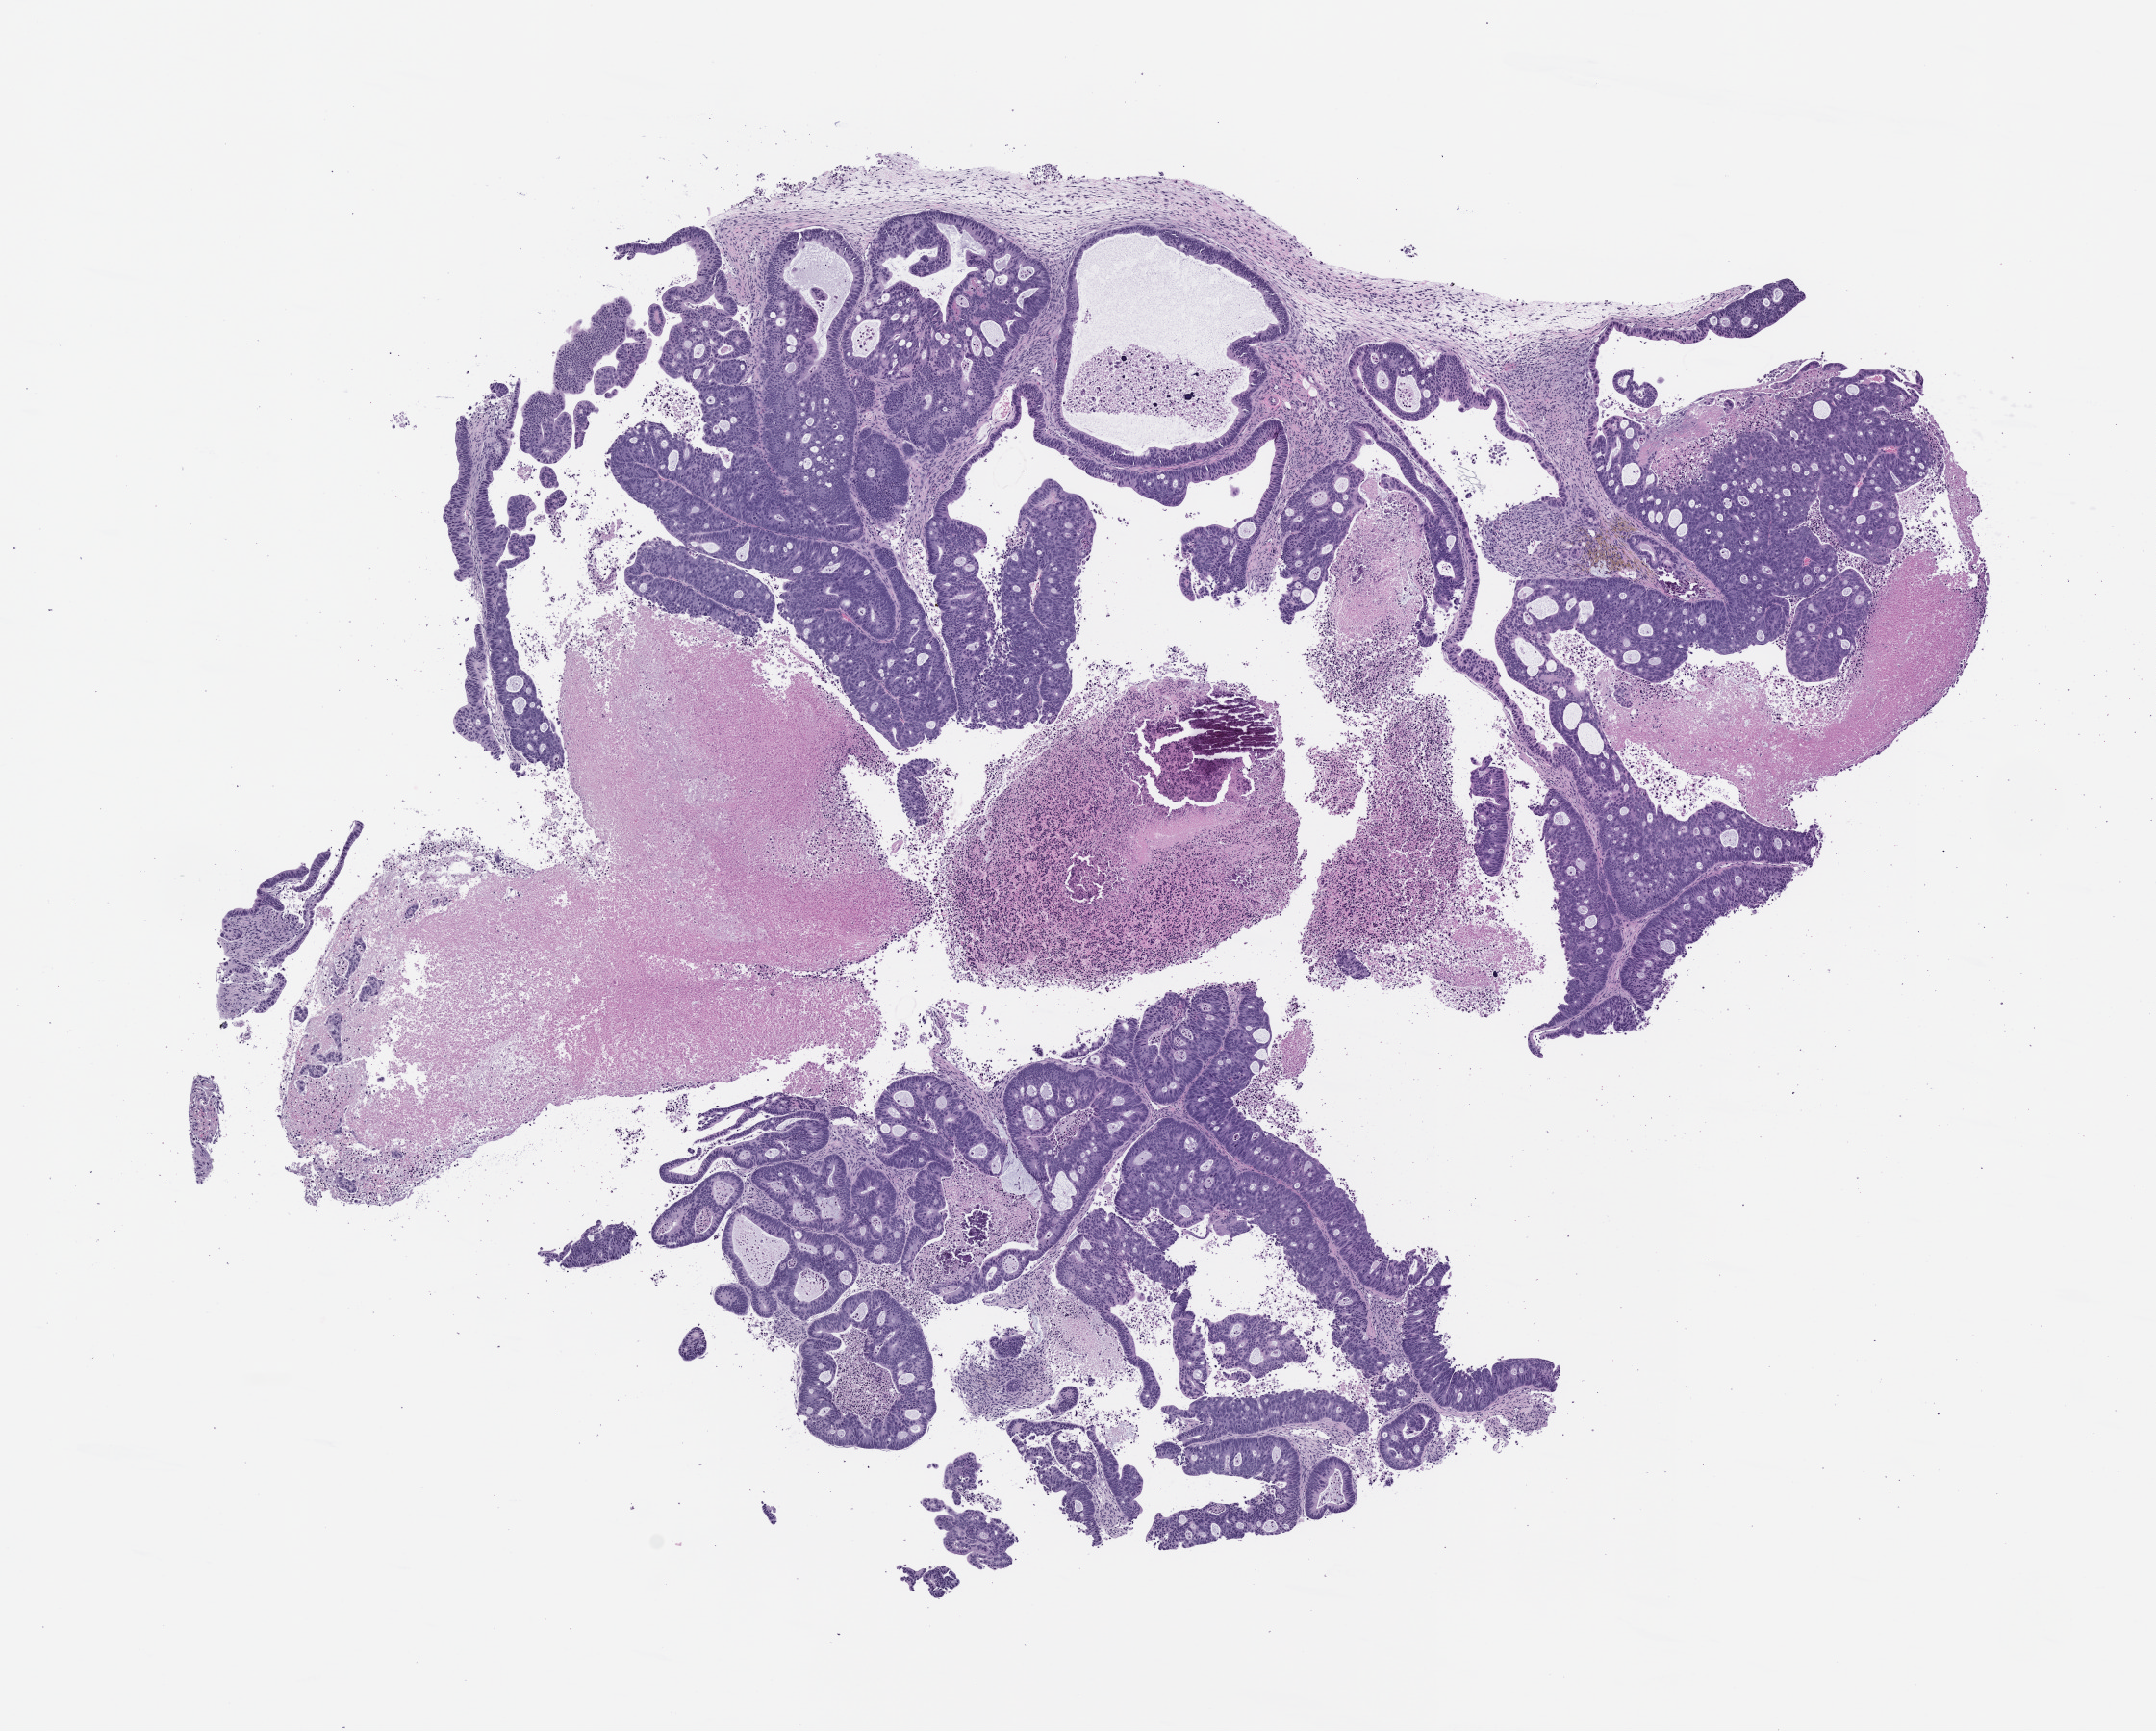
Whole-slide image, H&E: patient-derived xenograft (human tumor grown in a mouse), passage 1 — low-resolution overview of the scanned area, about 9.0 x 7.2 mm; formalin-fixed, paraffin-embedded (FFPE) tissue; tumor site category: gastrointestinal tract.
Originating patient diagnosis: Colorectal Carcinoma.